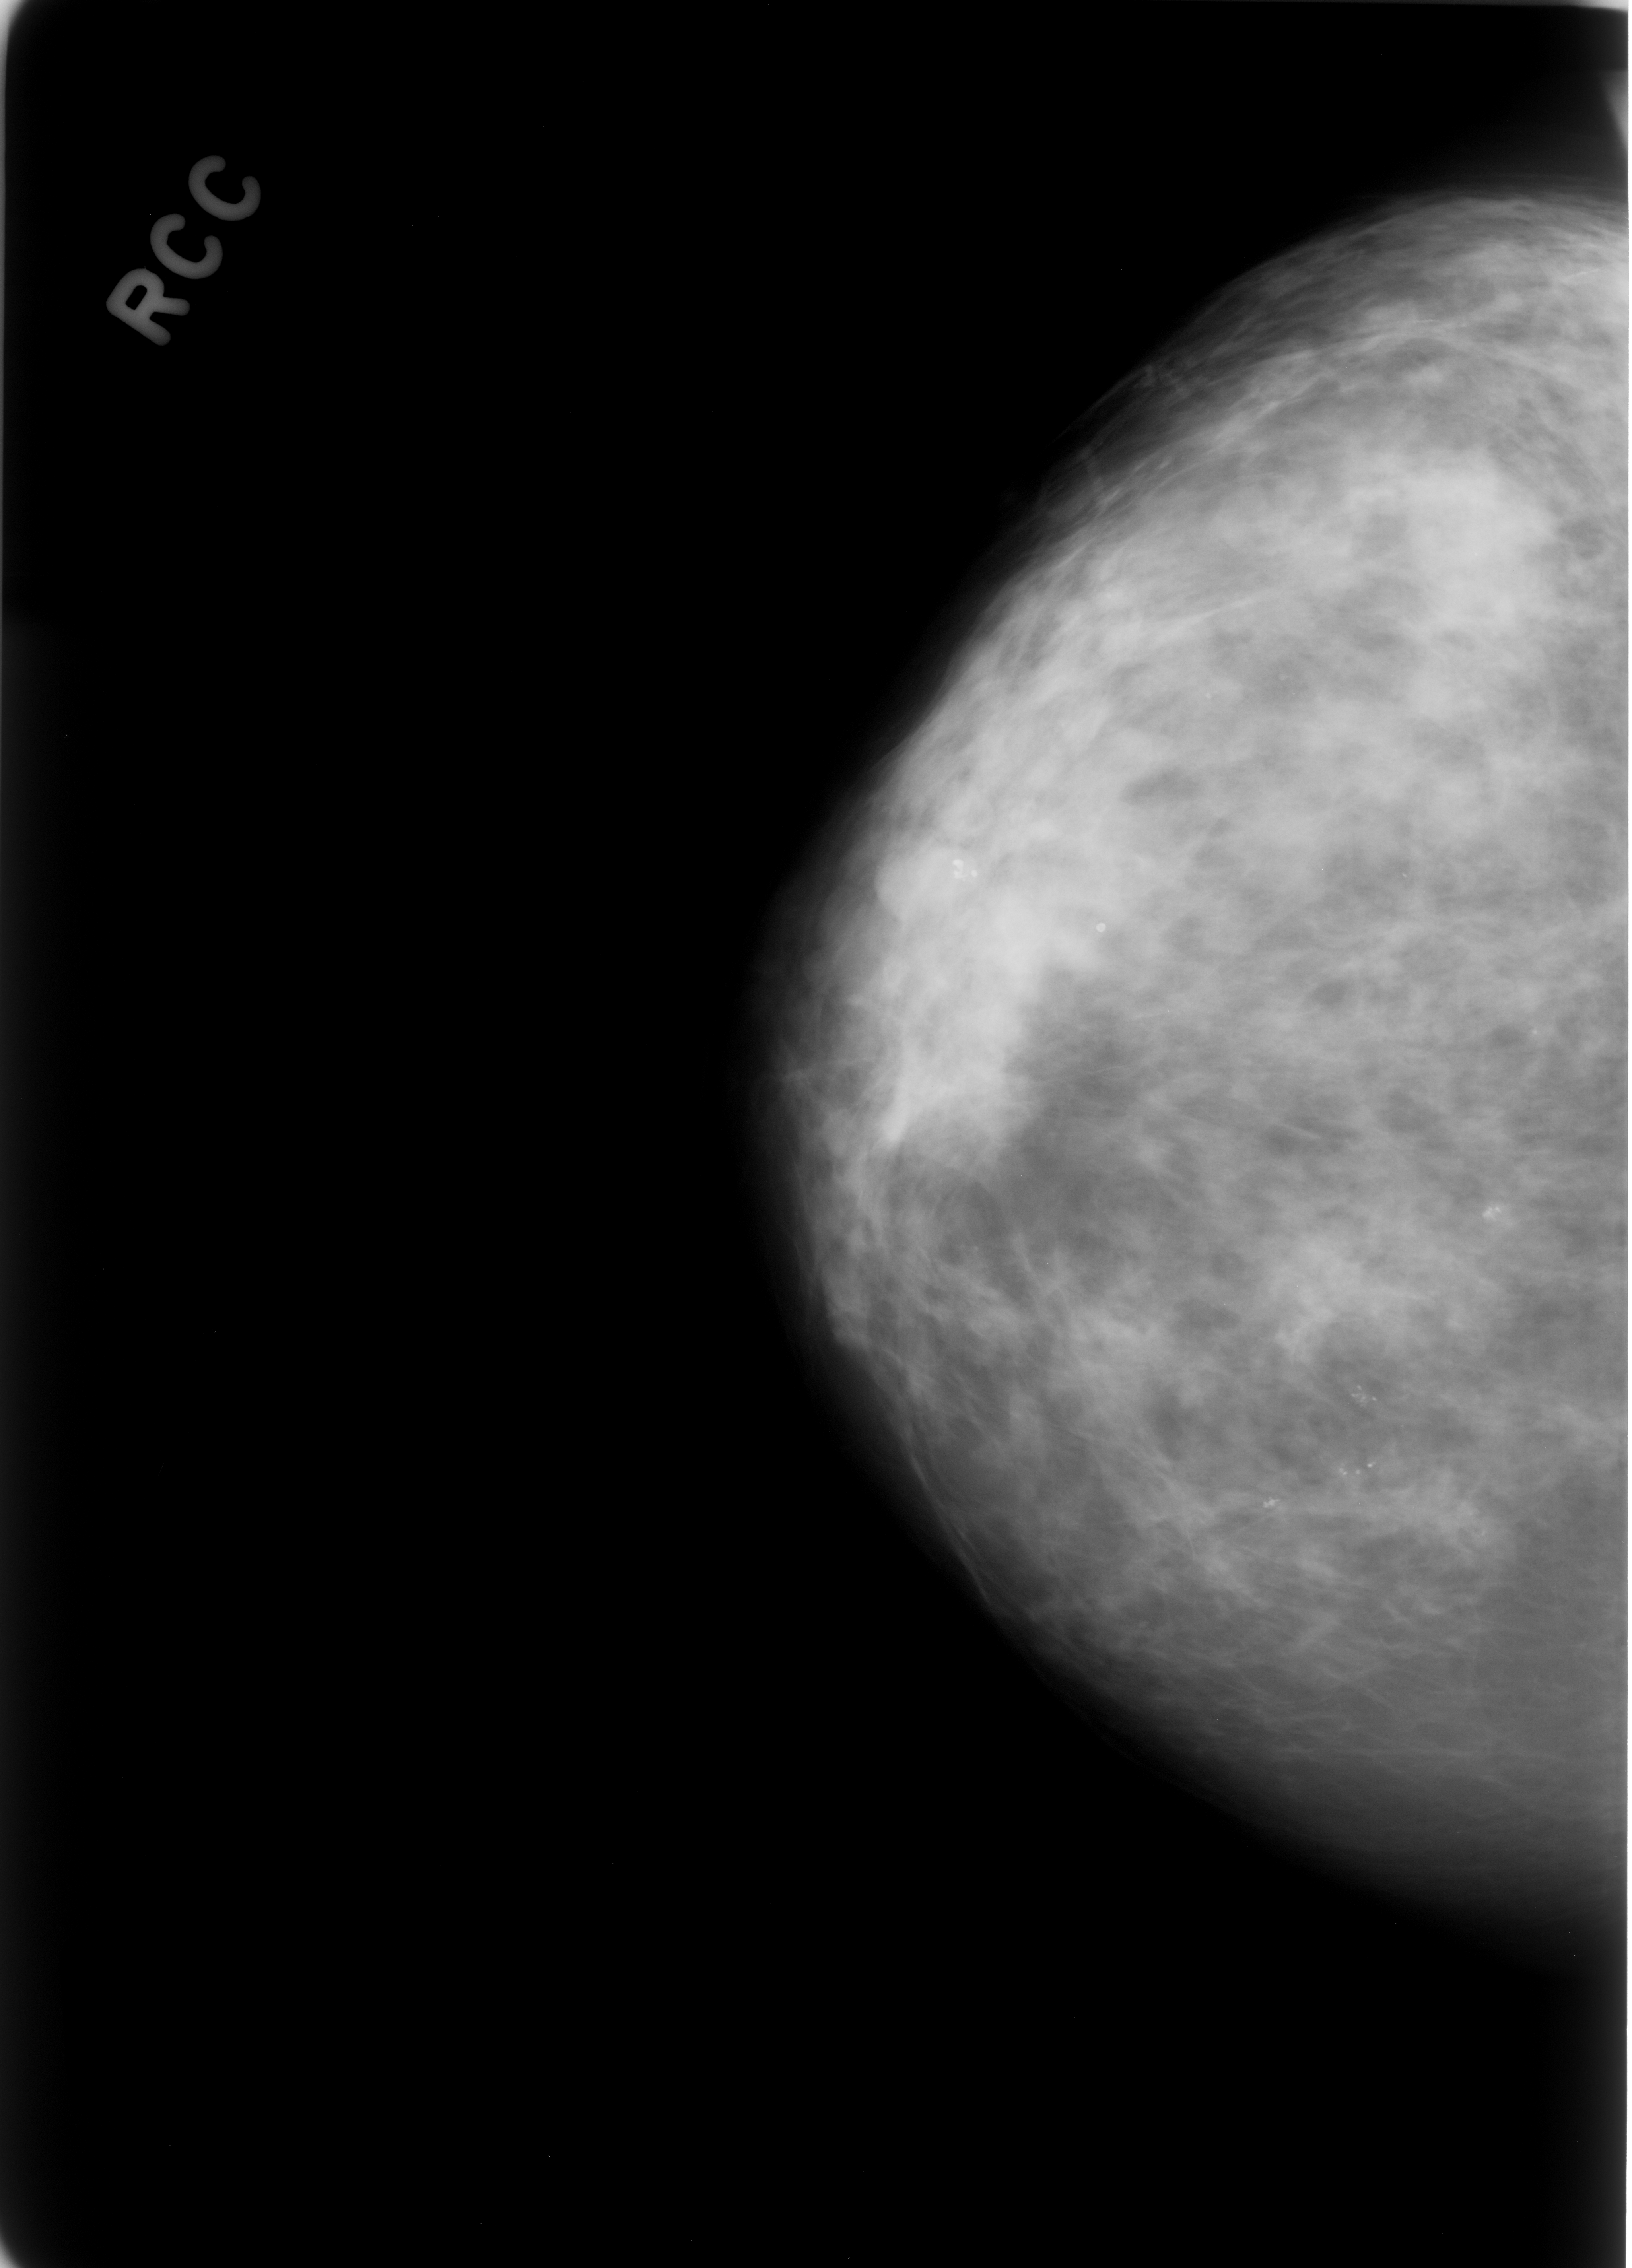
Digitized screen-film mammogram; right breast; CC view; breast composition: heterogeneously dense (BI-RADS density category 3 of 4); 1632 × 2268 image matrix.
Expert-marked regions of interest on this image (one box per marked abnormality):
- Finding 1 of 2: calcifications, morphology pleomorphic, distribution clustered; BI-RADS assessment category 4; subtlety rating 4 on a 1 (subtle) to 5 (obvious) scale; pathology result (as recorded, not read from the image): benign: bounding box <874,744,1019,933> (left, top, right, bottom; pixels)
- Finding 2 of 2: calcifications, morphology pleomorphic, distribution clustered; BI-RADS assessment category 4; subtlety rating 5 on a 1 (subtle) to 5 (obvious) scale; pathology (as recorded): benign: <1189,1335,1445,1610>